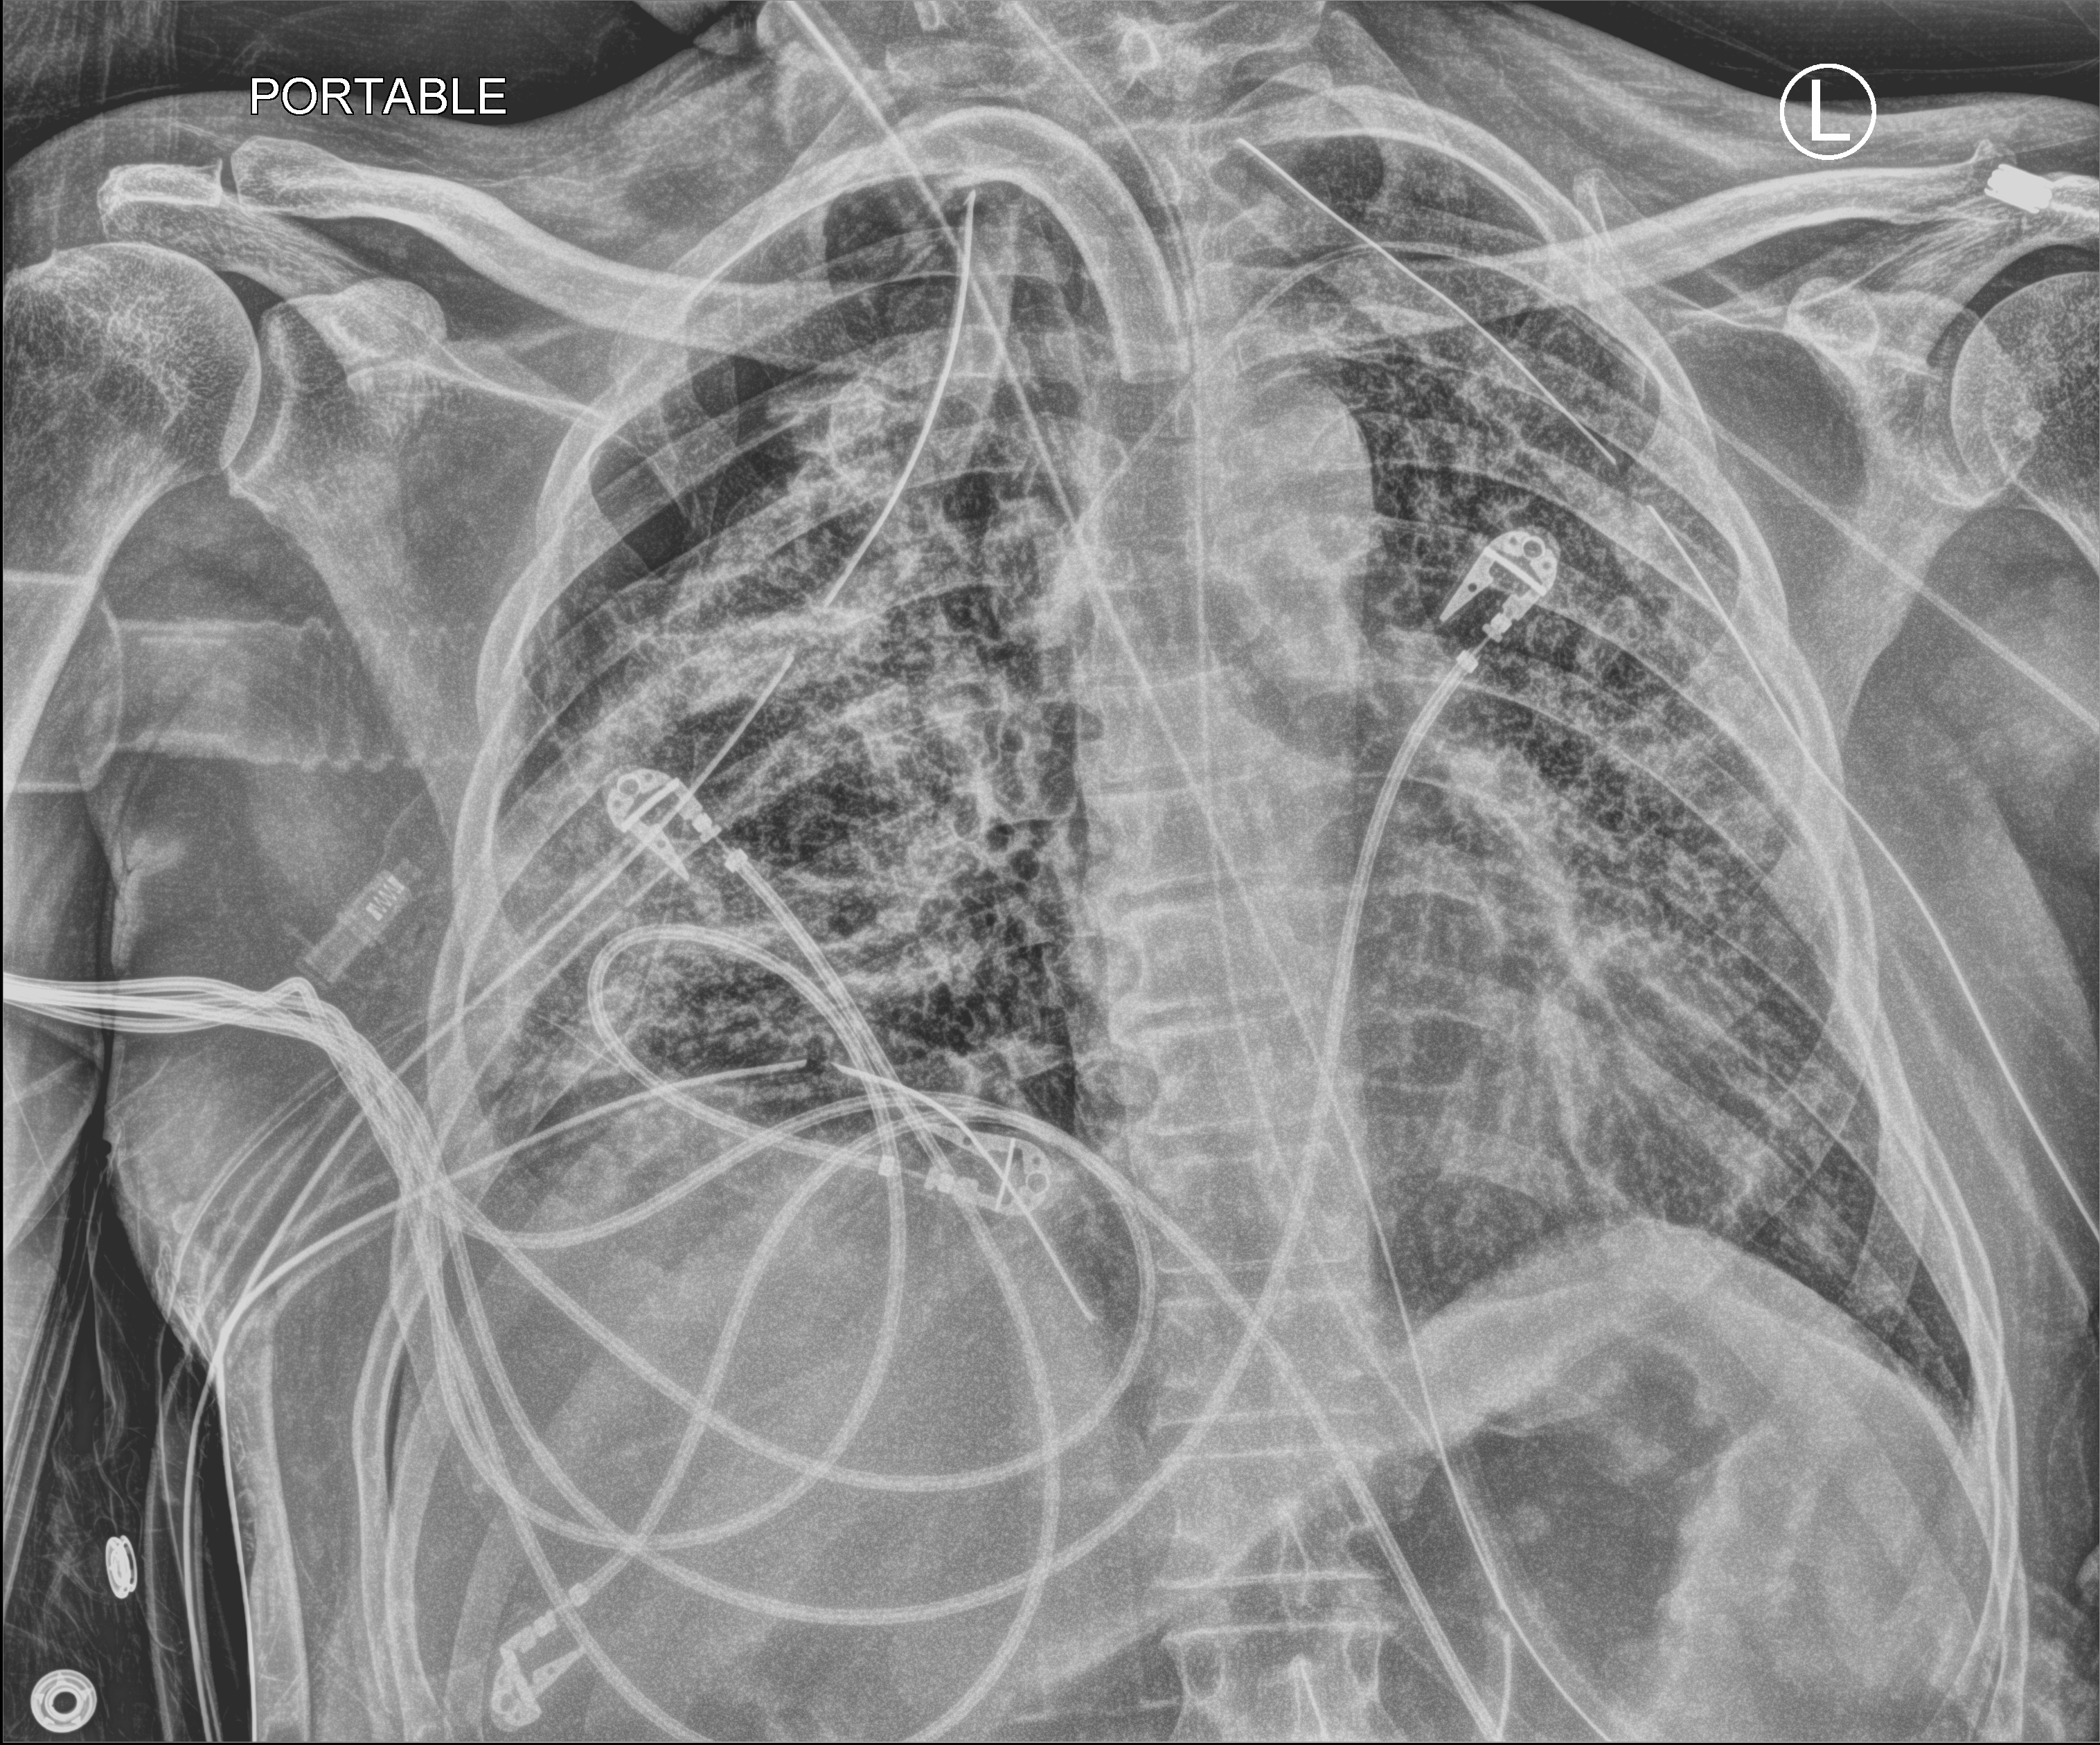
Bedside chest radiograph (computed radiography), anteroposterior (AP) projection. Male patient hospitalised with COVID-19, age 18–59 years.
Admission-level facts for this patient (not findings on this image; timing relative to this image not recorded):
- admitted to intensive care during this hospital stay: yes